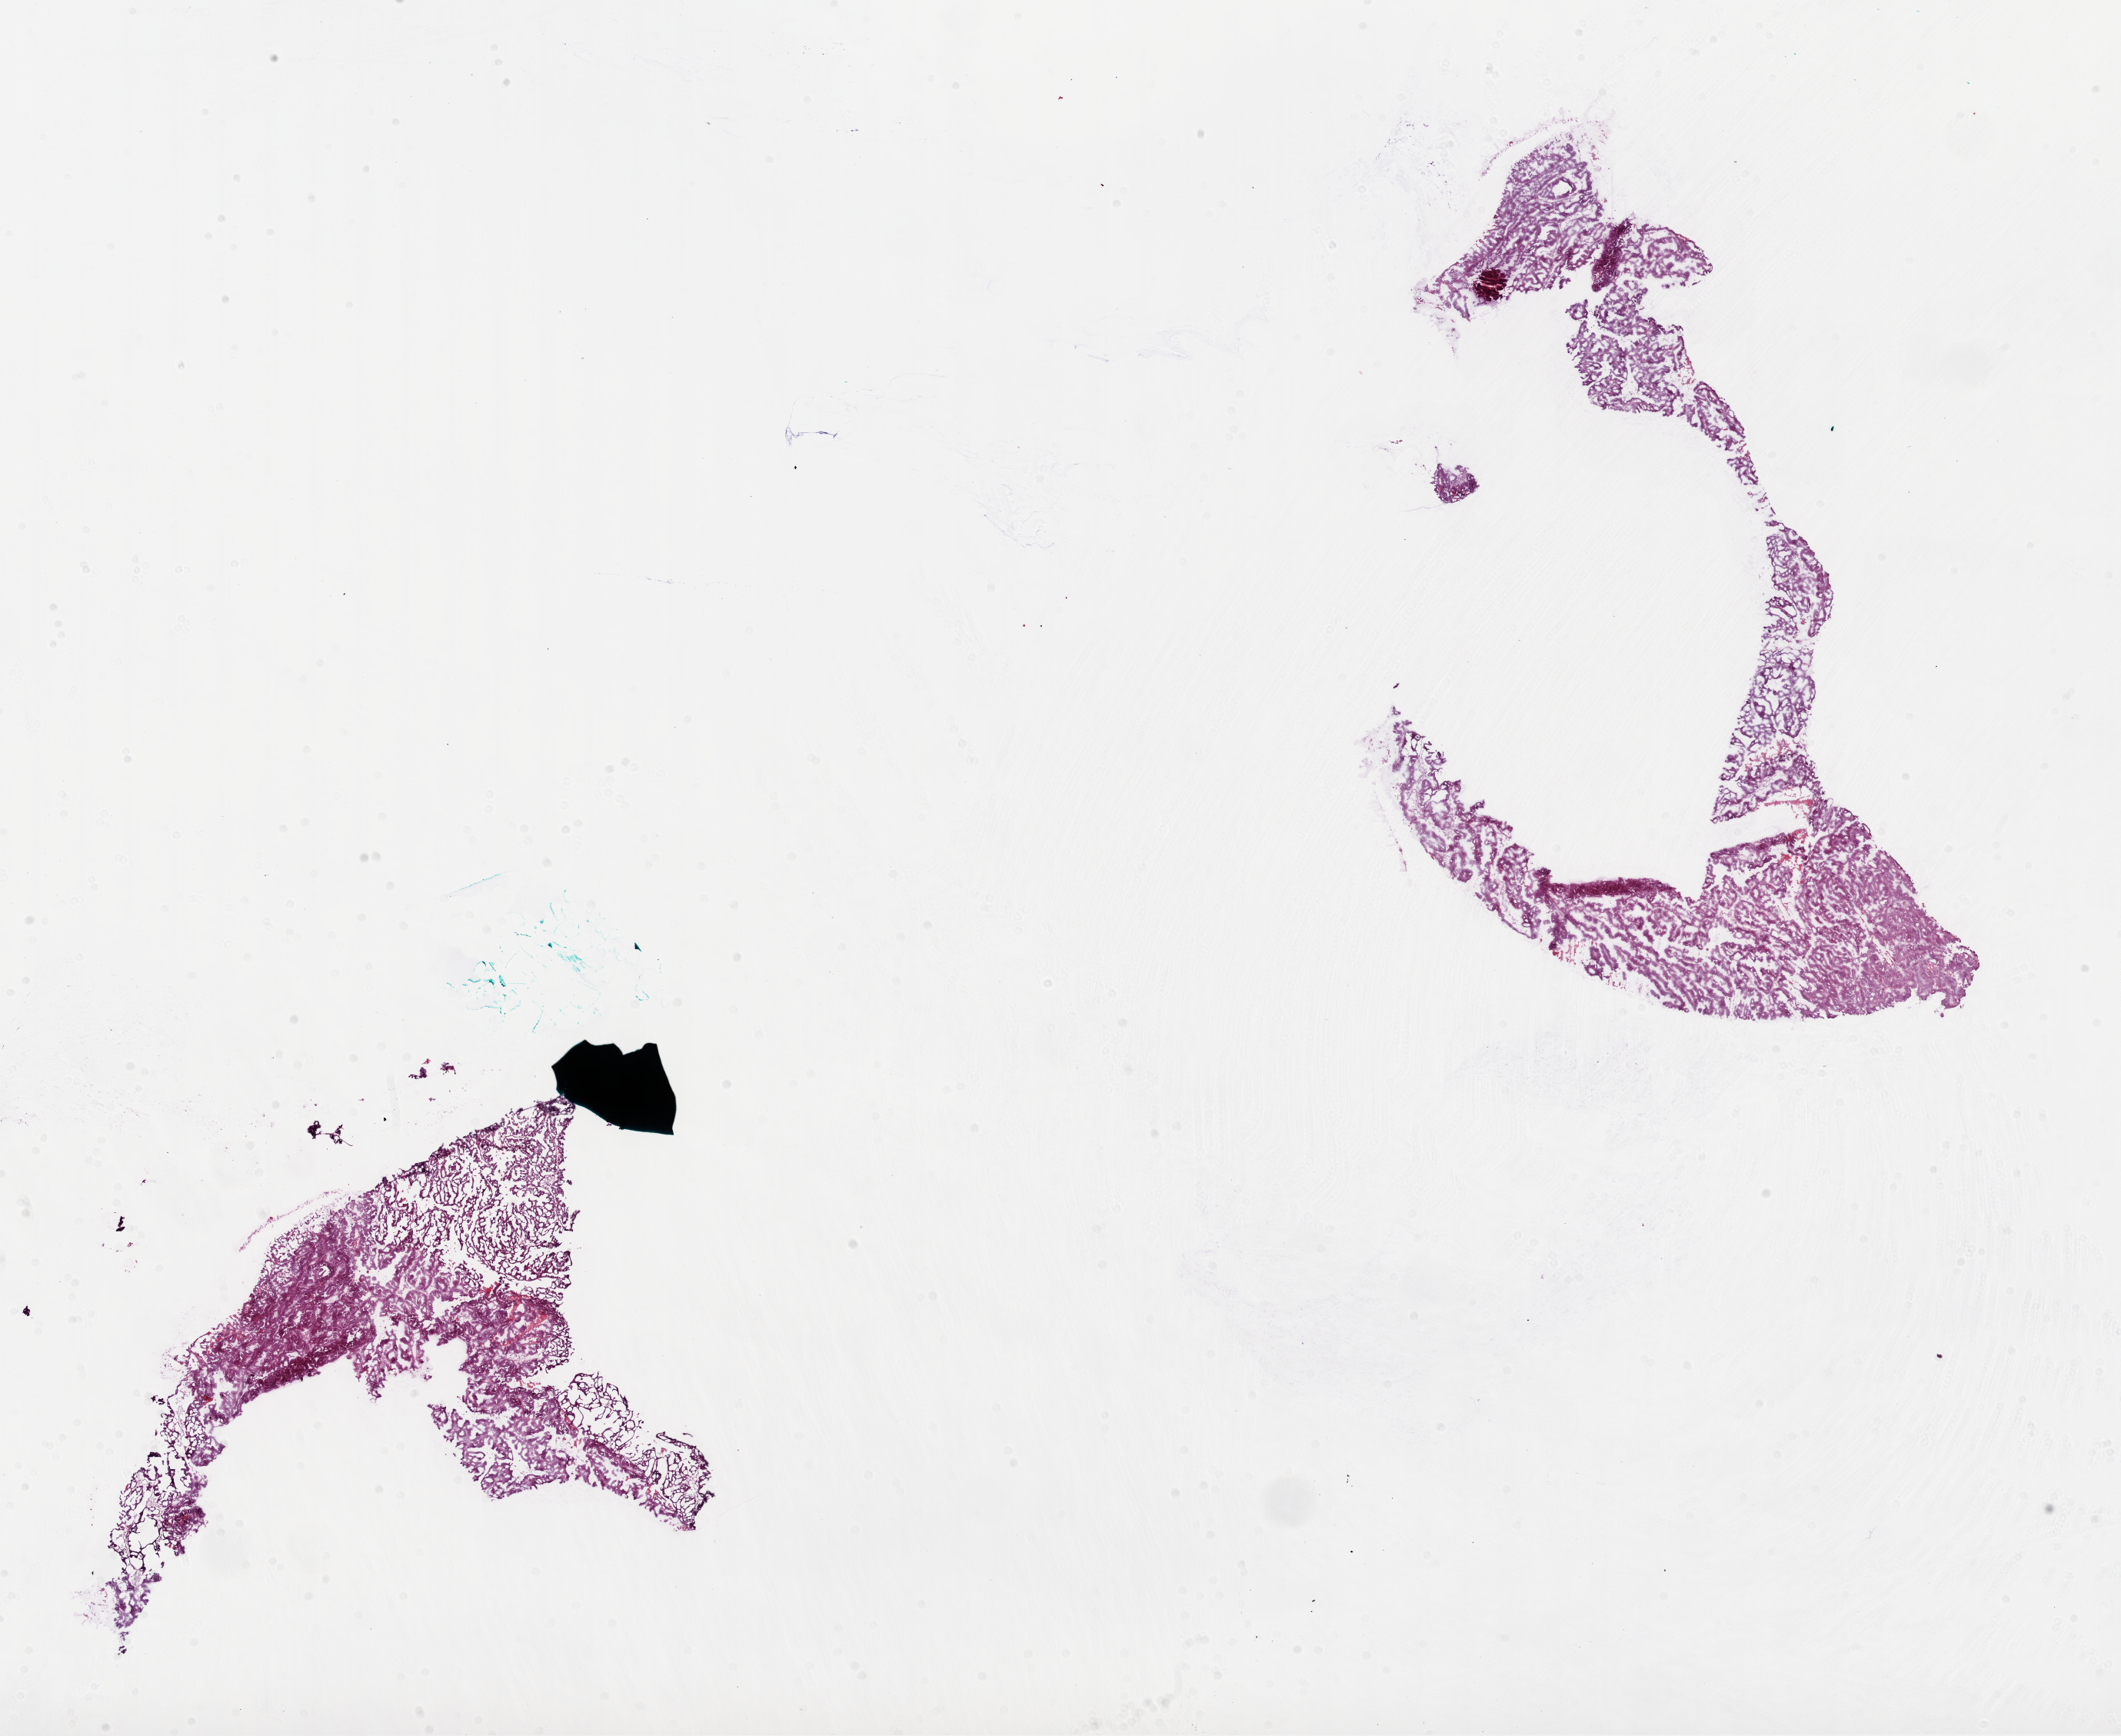
Digitized H&E-stained tissue section (whole slide), low-resolution overview of the scanned area, about 22.2 x 18.2 mm (slide scanned at 20x). Frozen section. Ovary, primary tumour sample. Female, age 50 years at initial diagnosis. Histologic grade: G3 (poorly differentiated). Slide review estimates, as recorded: tumour cells 90%, tumour nuclei 90%, normal cells 5%, stromal cells 5%, necrosis 0%.
* laterality: bilateral
* pathologic diagnosis: Serous cystadenocarcinoma, NOS
* FIGO stage: IIIC